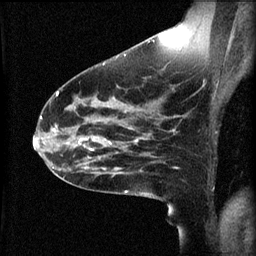
Breast MRI (dynamic contrast-enhanced), one sagittal slice; slice 33 of 60 in the series (ordered by position); 3 images stored at this slice position (order not interpretable as contrast timing); 1.5 T; TE 4.2 ms, TR 8.2 ms; 2 mm slice thickness; 256 × 256 image matrix. Patient: female, 49 years.
Outlined on this slice (semi-automatic segmentation, software-assisted and operator-edited):
- analysis volume of interest (the breast-tissue region the enhancement analysis was run in; not a lesion): bounding box <66,124,113,159> (left, top, right, bottom; pixels)
- tumour enhancement mask (voxels above the 70 % enhancement threshold inside the analysis volume of interest): <78,136,111,151>